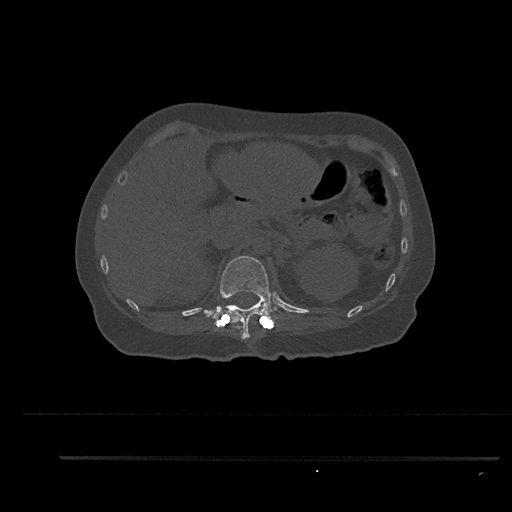
CT including the spine, one axial slice; position 256 of 797 along the scan axis; bone window (W 1800 / L 400 HU); 0.5 mm slice thickness; 512 × 512 image matrix, field of view 408 × 408 mm. Patient: female, 44 years. Case-level facts recorded for this patient, not image findings: primary cancer: renal.
Annotated regions visible in this slice (semi-automatic segmentation, software-assisted and operator-edited):
- T12 vertebra: bounding box [x1, y1, x2, y2] px = [204, 256, 277, 339]